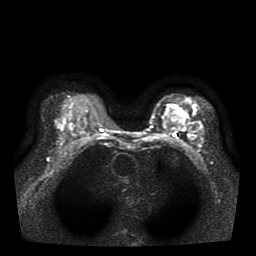
Breast MRI, one axial slice. Position 26 of 39 along the scan axis. Diffusion-weighted series; image 2 of 4 stored at this slice position (different b-values; order by instance number). 1.5 T. 256 × 256 image matrix, field of view 330 × 330 mm. Female patient.
Outlined on this slice (outlined manually by an expert reader):
- tumour on diffusion-weighted imaging: box from (x=174, y=108) to (x=187, y=117) px